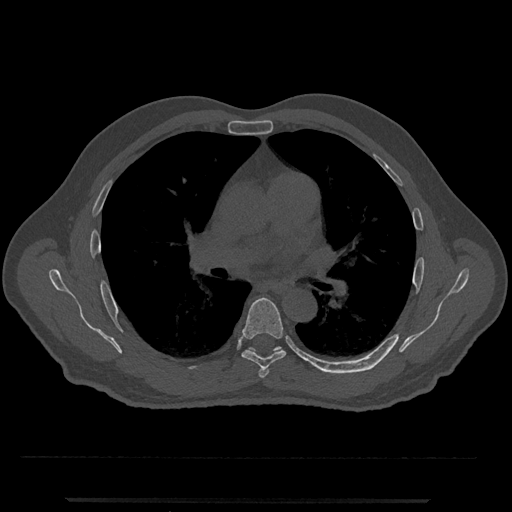
CT including the spine, one axial slice; position 731 of 797 along the scan axis; 120 kVp; bone window (W 1800 / L 400 HU); 0.5 mm slice thickness; 512 × 512 image matrix, field of view 419 × 419 mm. Patient: male, 63 years. From the clinical record (not read from this slice): primary cancer: prostate.
Annotated regions visible in this slice (semi-automatically segmented with operator editing):
- T5 vertebra: bounding box <258,369,269,378> (left, top, right, bottom; pixels)
- T6 vertebra: <241,298,286,369>
- T7 vertebra: <248,346,329,373>